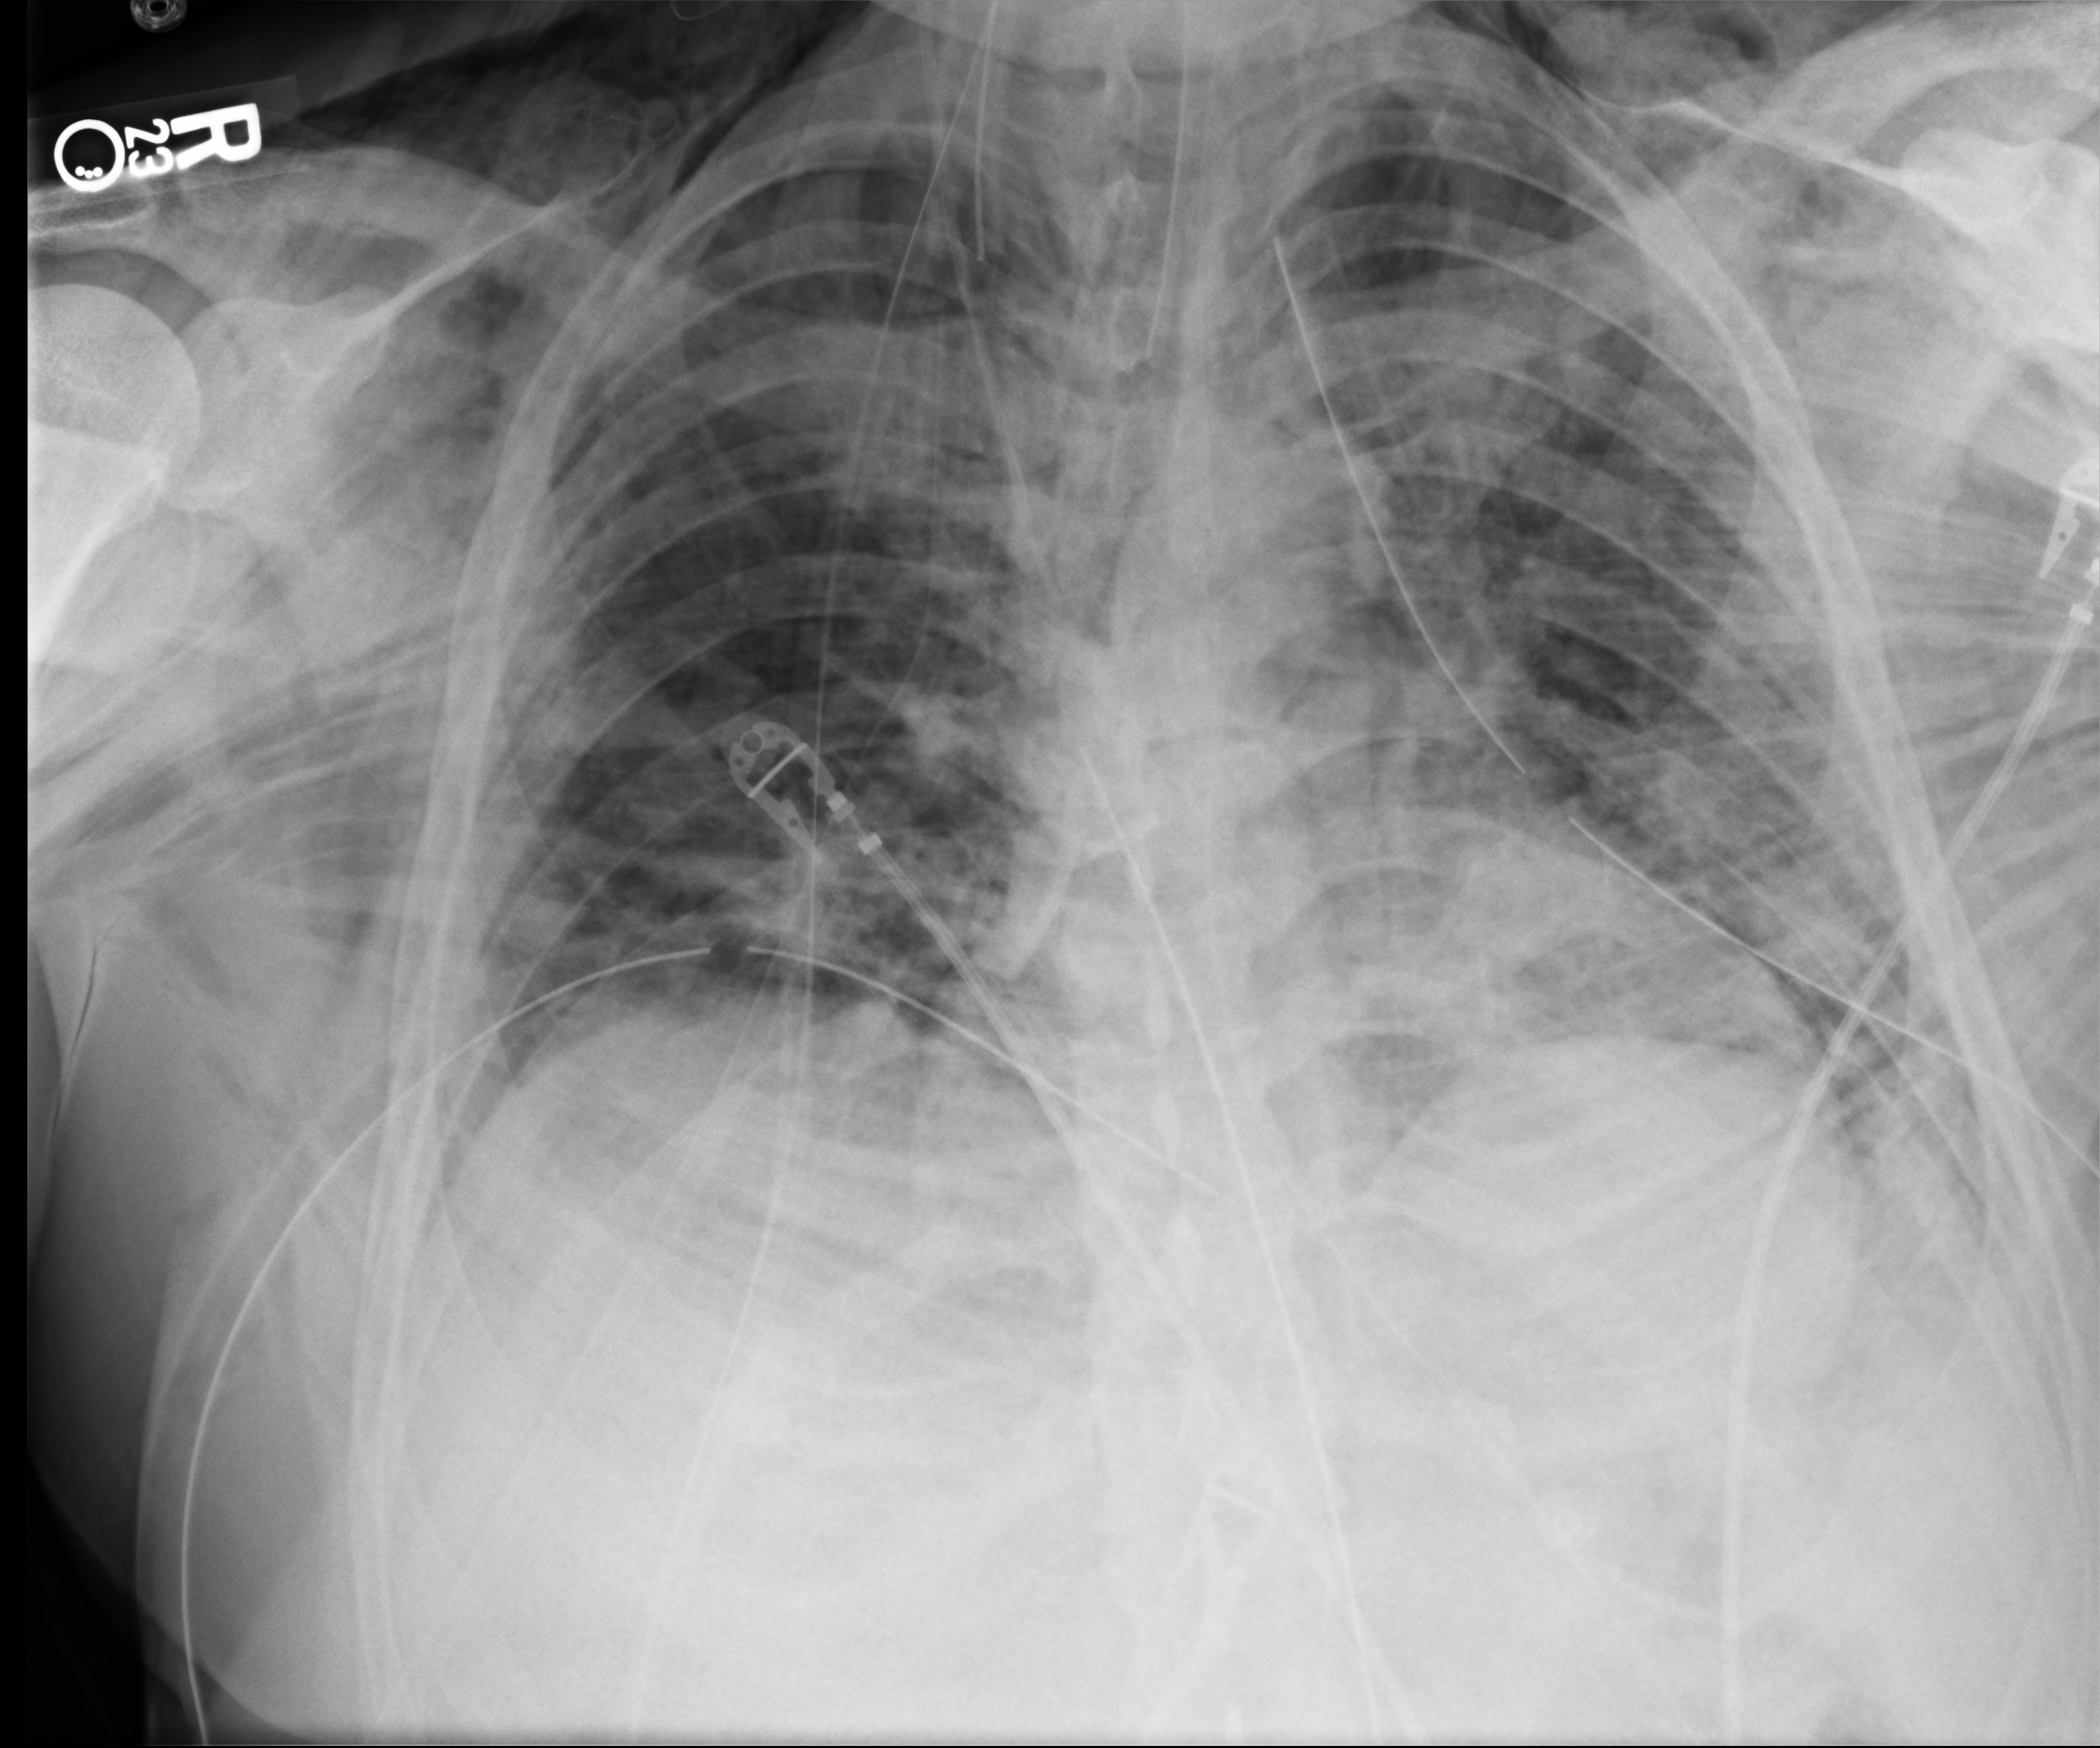
Bedside chest radiograph (computed radiography); anteroposterior (AP) projection. Male patient hospitalised with COVID-19, age 18–59 years.
Admission-level facts for this patient (not findings on this image; timing relative to this image not recorded): admitted to intensive care during this hospital stay: yes; mechanically ventilated during this hospital stay: yes.